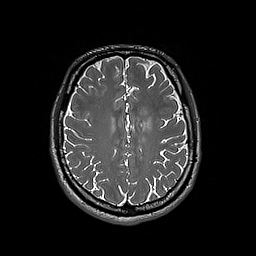
Brain MRI from a brain-tumour surgery series, one axial slice. 256 × 256 image matrix. Case-level facts recorded for this patient, not image findings: histopathology: Oligodendroglioma; WHO grade: 3; IDH mutation: yes; tumour location: Left Frontal.
Structures marked on this image (outlined manually by an expert reader):
- tumour: box from (x=139, y=118) to (x=153, y=130) px